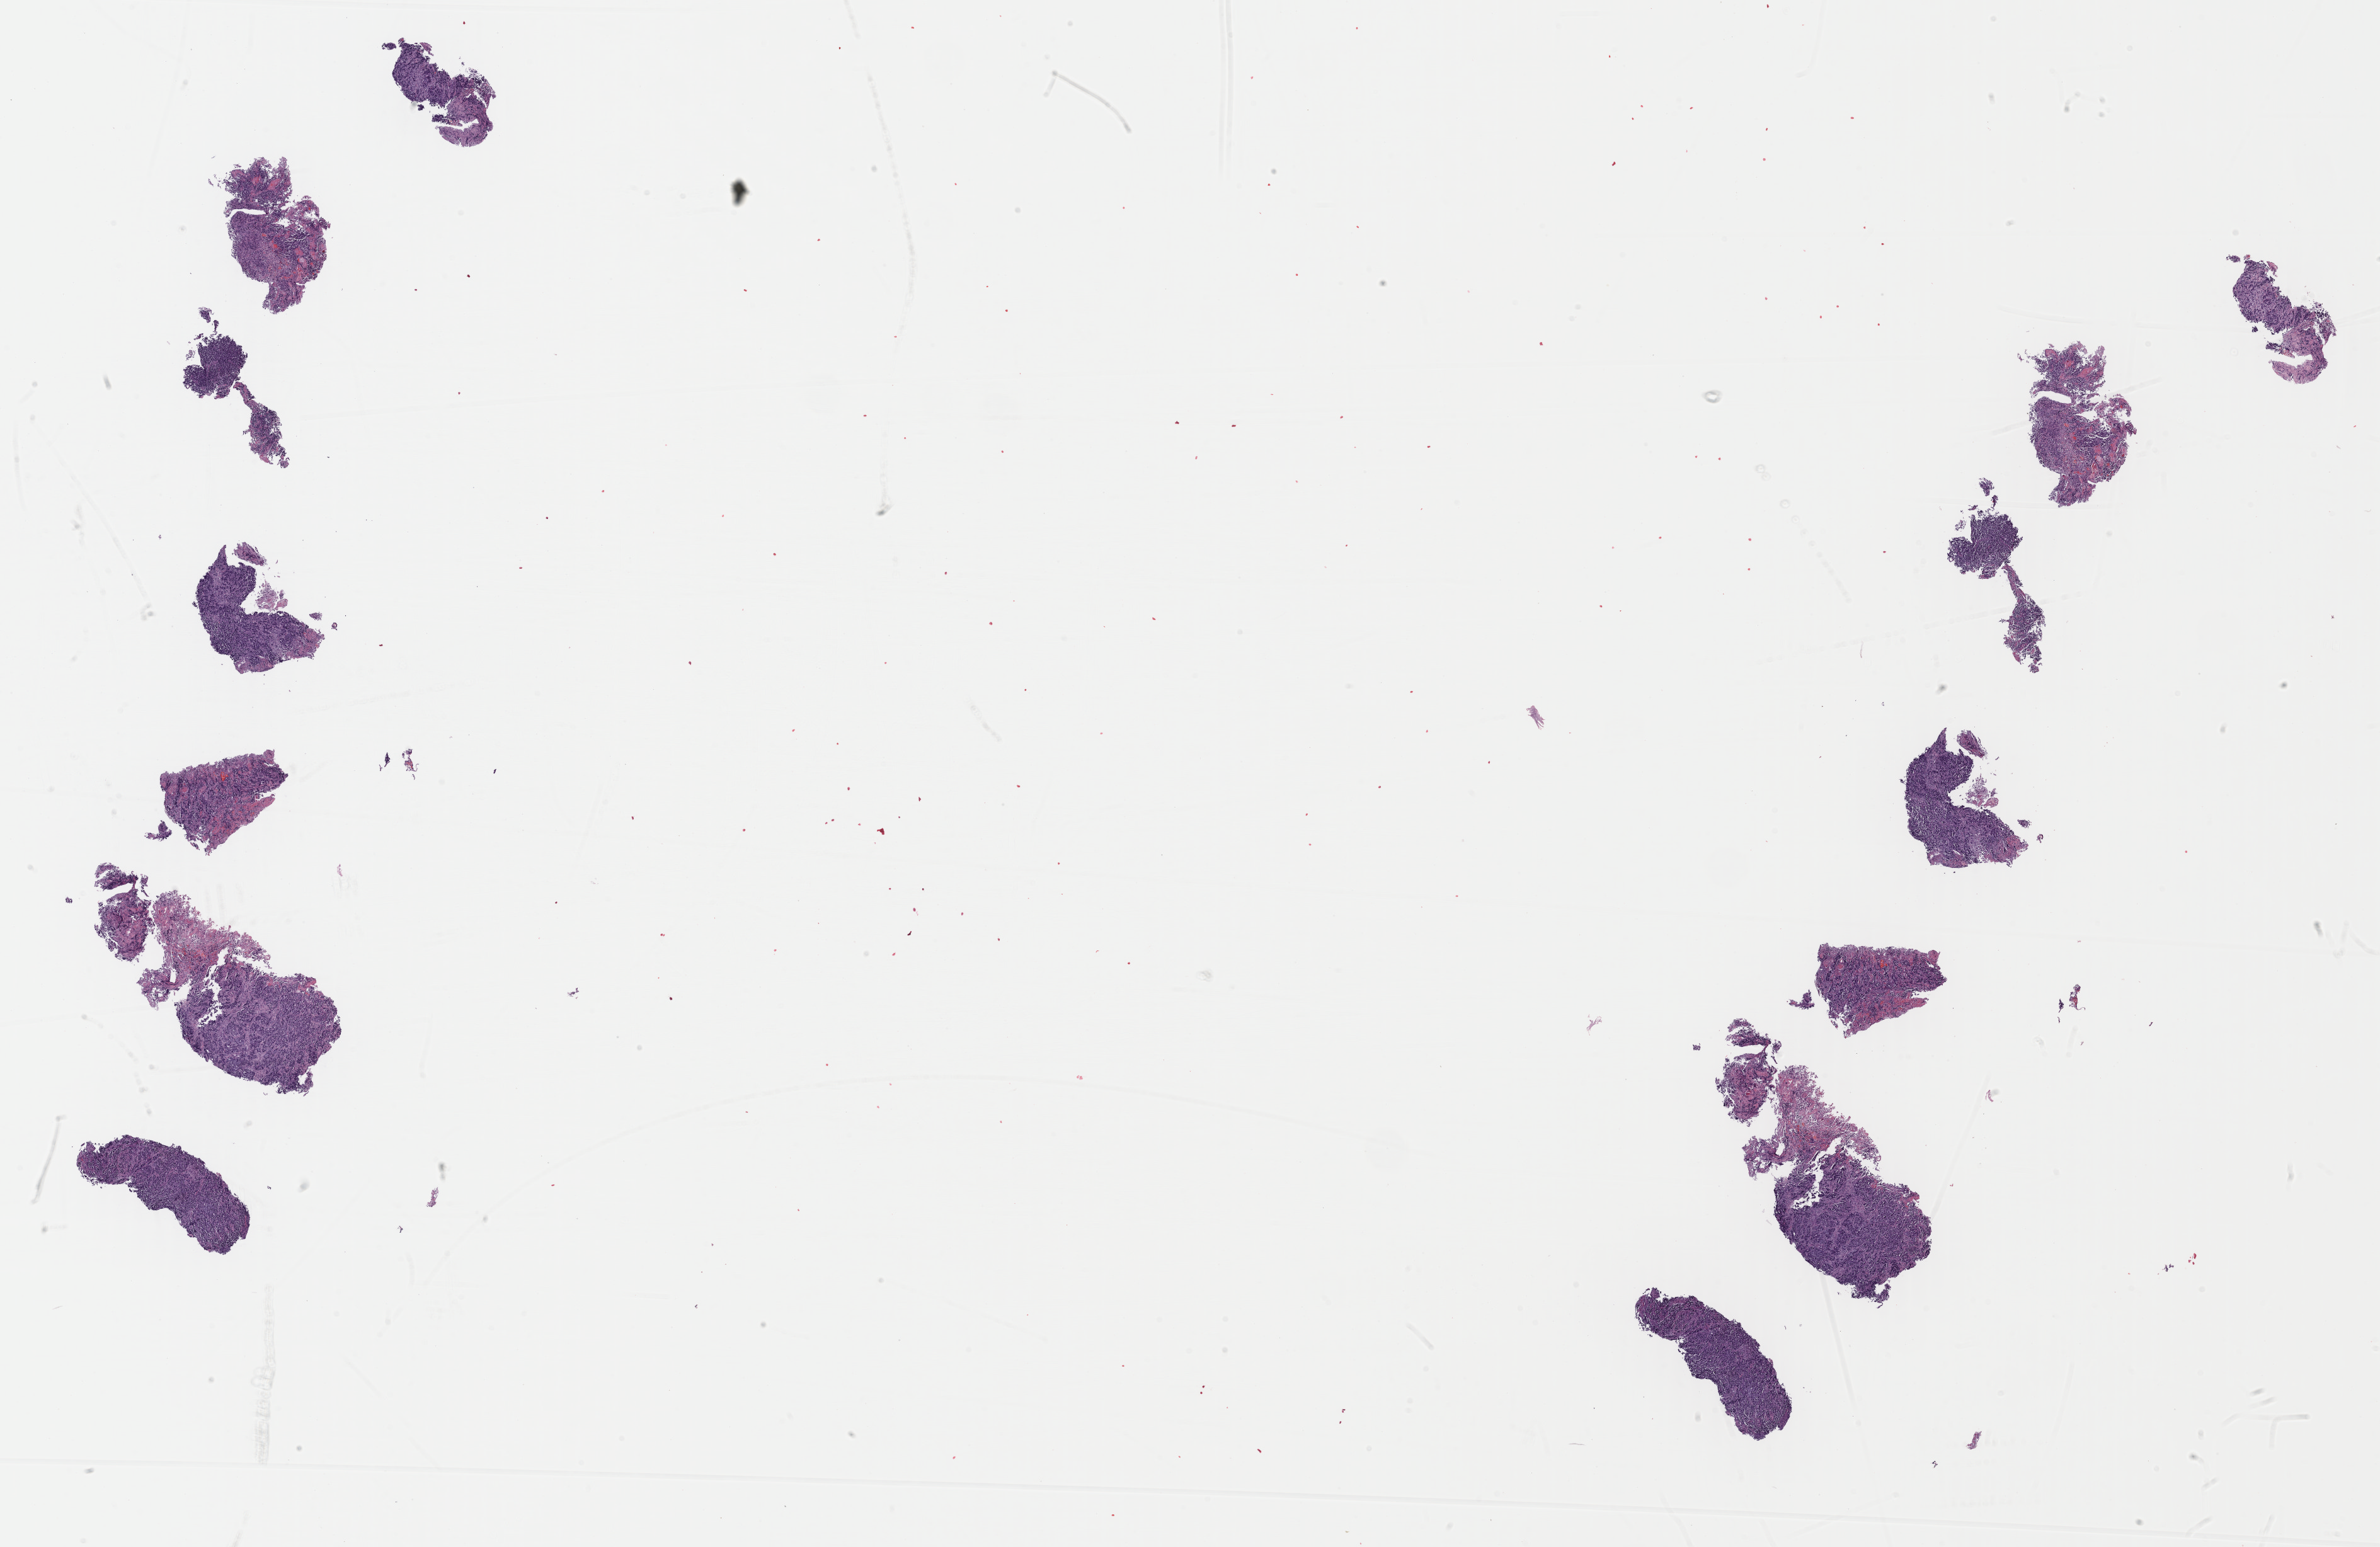
H&E-stained whole-slide image — whole scanned area (about 29.8 x 19.4 mm, acquisition: 40x scan) shown as a low-resolution overview. Formalin-fixed paraffin-embedded (FFPE) diagnostic section. Primary tumour sample from the esophagus. Patient: male, age at initial diagnosis 58 years. Histologic grade: G3 (poorly differentiated). Pathologist review of this section (percent, as recorded): tumour cells 80%, tumour nuclei 80%, normal cells 0%, stromal cells 20%, necrosis 0%. Infiltration values recorded for this section: lymphocyte infiltration 40%, monocyte infiltration 20%, neutrophil infiltration 20%.
* pathologic diagnosis: Adenocarcinoma, NOS